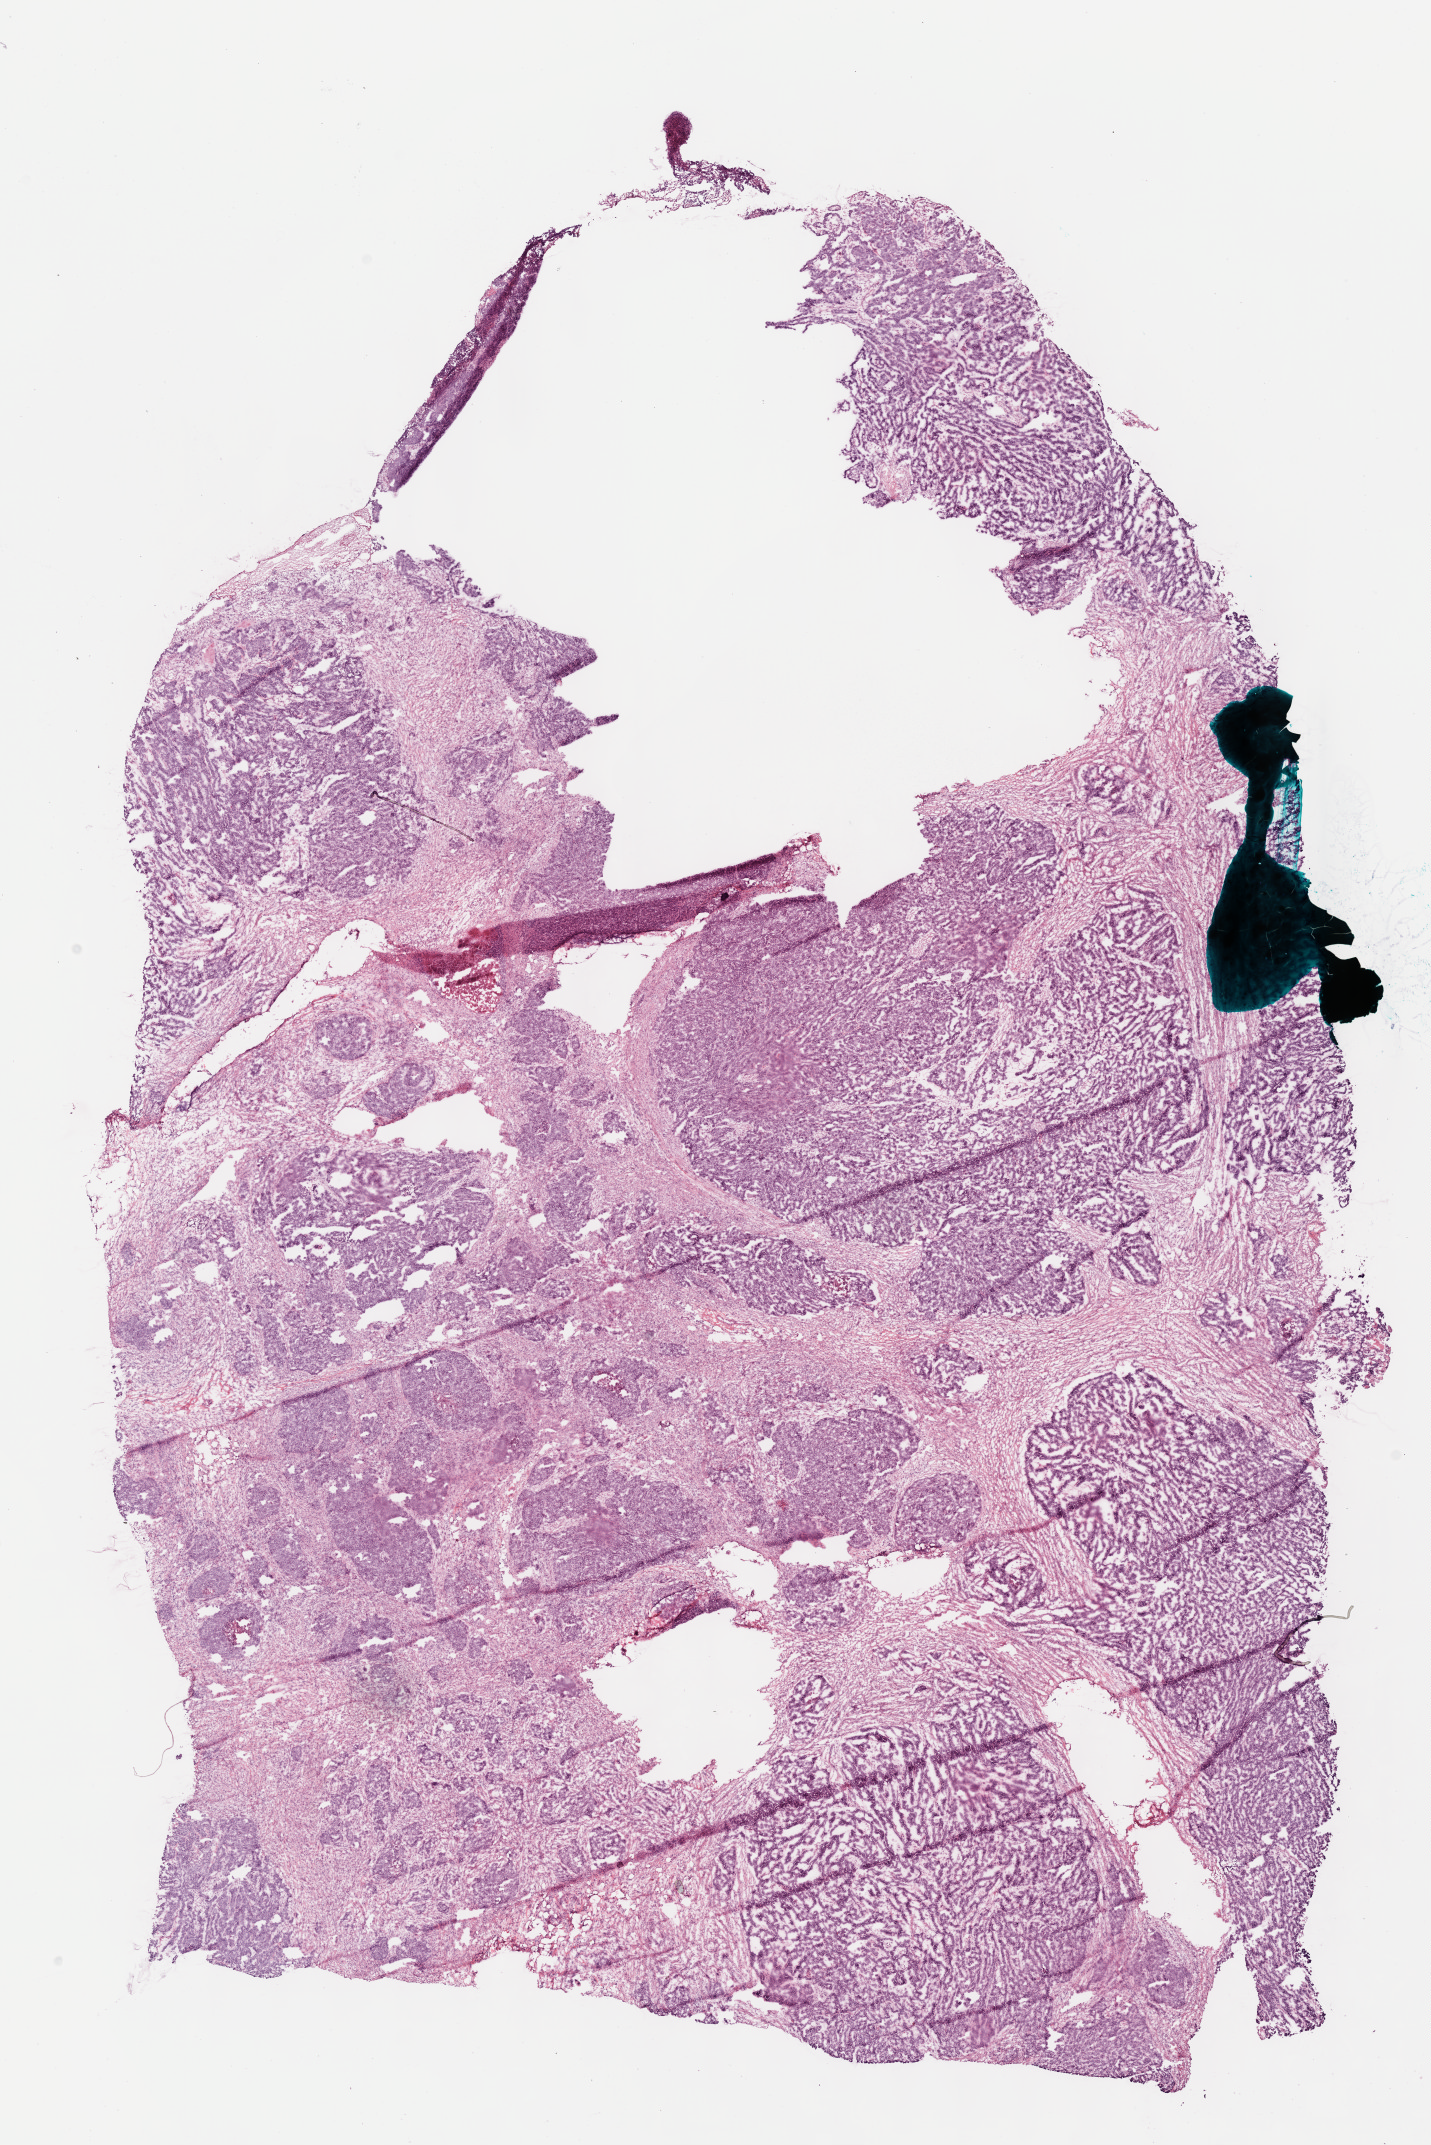
Digitized H&E tissue section (whole slide), a low-resolution overview of the entire scanned area, about 11.6 x 17.3 mm (slide scanned at 40x), frozen section, sample: primary tumour, ovary. Patient: female, age at initial diagnosis 48 years. Histologic grade: G3 (poorly differentiated). Composition of this section per pathologist review: tumour cells 79%, tumour nuclei 80%, normal cells 0%, stromal cells 20%, necrosis 1%.
Diagnosis: Serous cystadenocarcinoma, NOS. Laterality: bilateral. FIGO stage: IIIC.